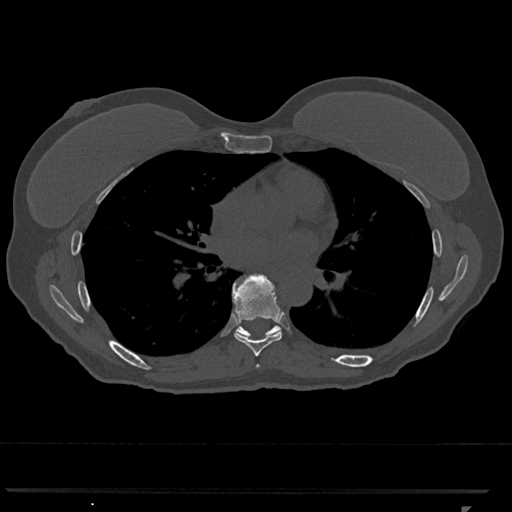
CT including the spine, one axial slice; slice 700 of 793 in the series (ordered by position); reconstruction kernel Br40s/3; bone window (W 1800 / L 400 HU); 0.5 mm slice thickness; 512 × 512 image matrix, field of view 380 × 380 mm. Female patient, age 62 years. Case-level facts recorded for this patient, not image findings: primary cancer: renal.
Outlined on this slice (semi-automatically segmented with operator editing):
- T6 vertebra: bounding box (x1, y1, x2, y2) in pixels: (257, 365, 259, 367)
- T7 vertebra: (232, 274, 282, 357)
- T8 vertebra: (236, 325, 280, 336)